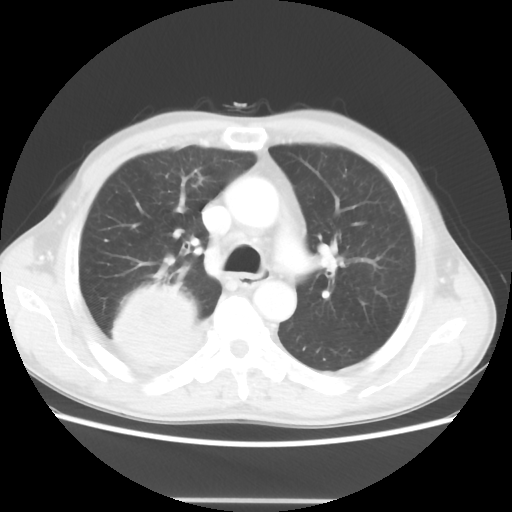
Chest CT, one axial slice; position 33 of 48 along the scan axis; reconstruction kernel STANDARD; lung window (W 1500 / L -600 HU); 5 mm slice thickness; 512 × 512 image matrix, field of view 361 × 361 mm. Male patient, age 66 years. Case-level facts recorded for this patient, not image findings: clinical TNM (as recorded): T4 N1 M1.
Annotated regions visible in this slice (bounding box drawn by a radiologist):
- lung tumour (recorded histology: small cell carcinoma): bounding box [x1, y1, x2, y2] px = [100, 279, 204, 377]